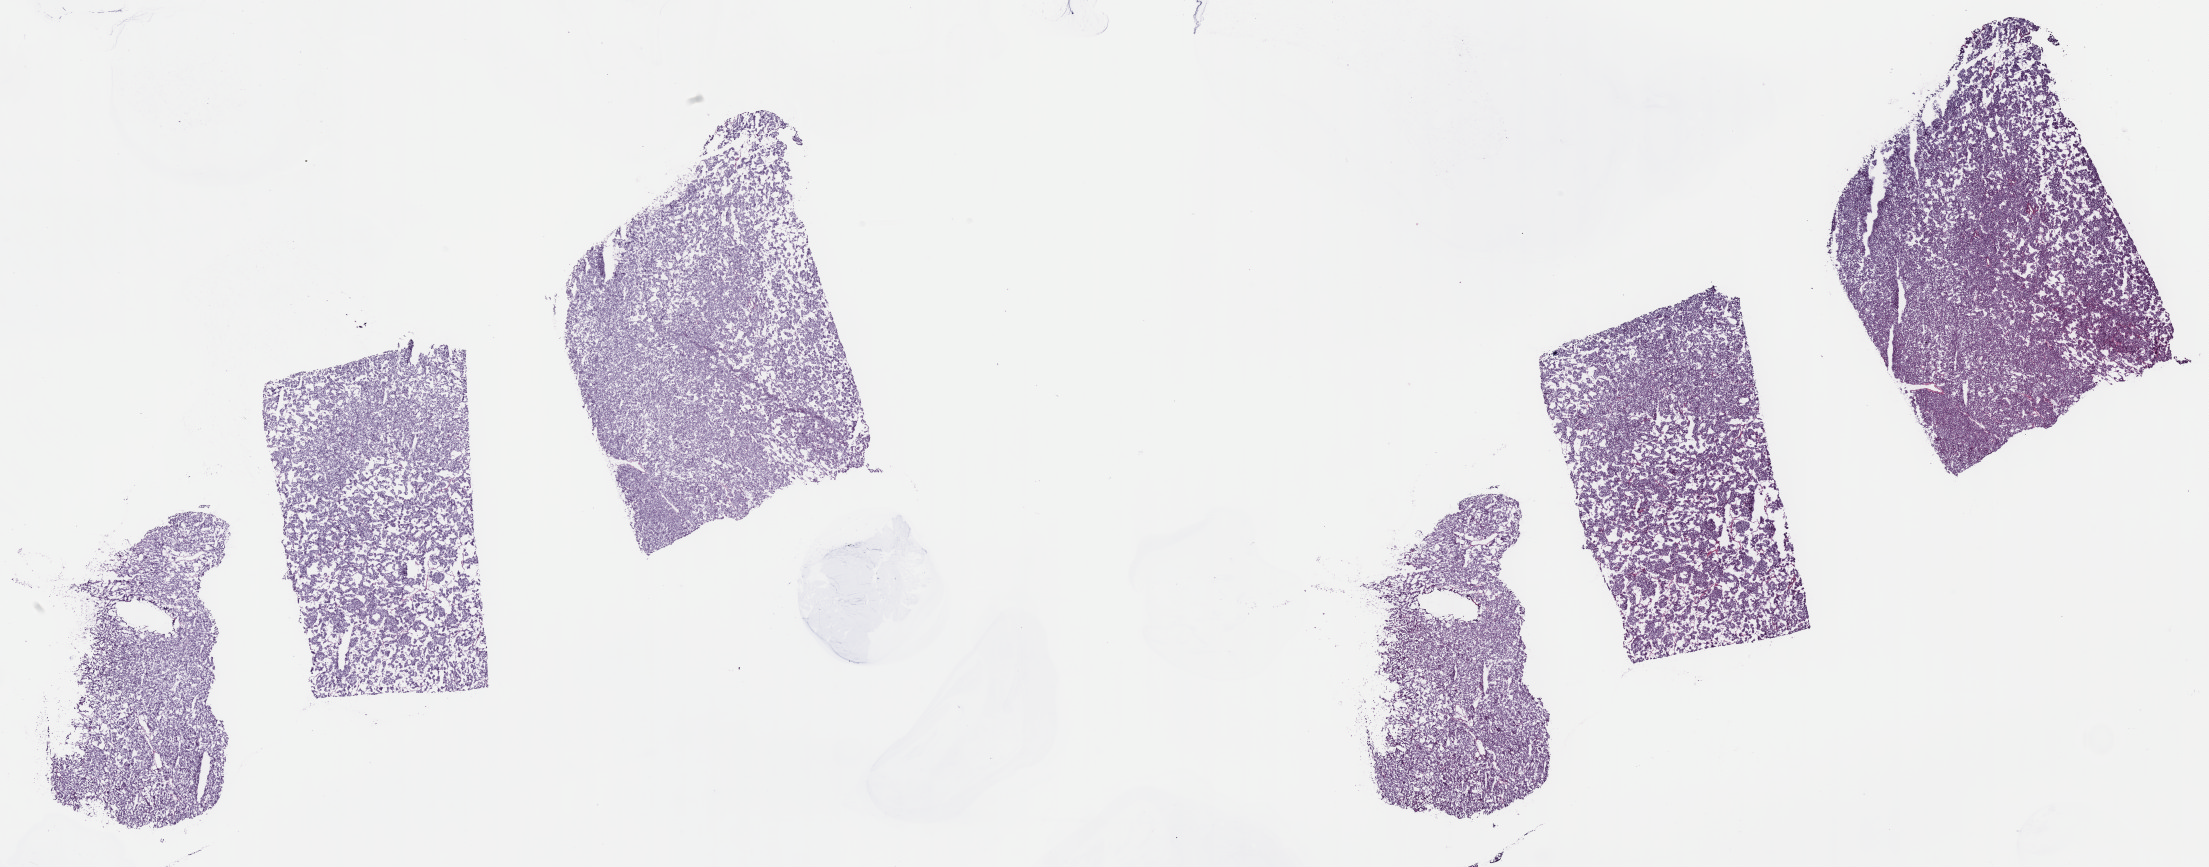
H&E-stained whole-slide image, shown as a low-resolution overview of the whole scanned area (about 35.7 x 14.0 mm). Frozen section from the top of the tissue portion. Pancreas, primary tumour sample. Patient: male, age at initial diagnosis 65 years. Histologic grade: G1 (well differentiated). Slide review estimates, as recorded: tumour cells 90%, tumour nuclei 90%, normal cells 0%, stromal cells 10%, necrosis 0%. Inflammatory infiltration, as recorded: lymphocyte infiltration 40%, monocyte infiltration 20%, neutrophil infiltration 20%.
Lymph nodes positive (case pathology): 0 of 16 examined. TNM: T2 N0 MX. AJCC pathologic stage: IB (6th edition). Pathologic diagnosis: Neuroendocrine carcinoma, NOS (head of pancreas).